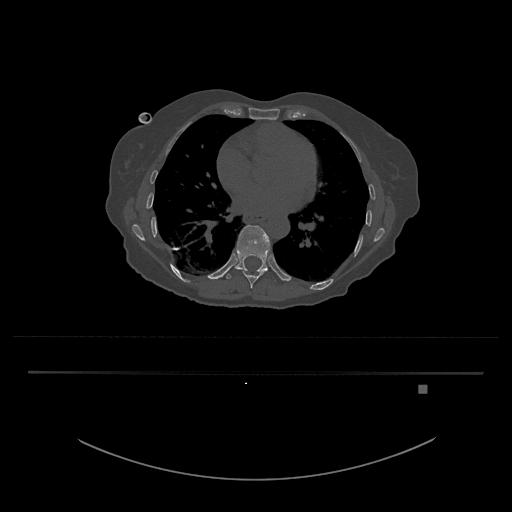
CT including the spine, one axial slice; position 736 of 797 along the scan axis; reconstruction kernel Br40s/3; 120 kVp; bone window (W 1800 / L 400 HU); 512 × 512 image matrix, field of view 500 × 500 mm. Patient: female, 57 years. From the clinical record (not read from this slice): primary cancer: cervical.
Annotated regions visible in this slice (semi-automatic segmentation, software-assisted and operator-edited):
- T10 vertebra: box from (x=224, y=225) to (x=276, y=281) px
- T9 vertebra: (x=246, y=273)–(x=263, y=289)